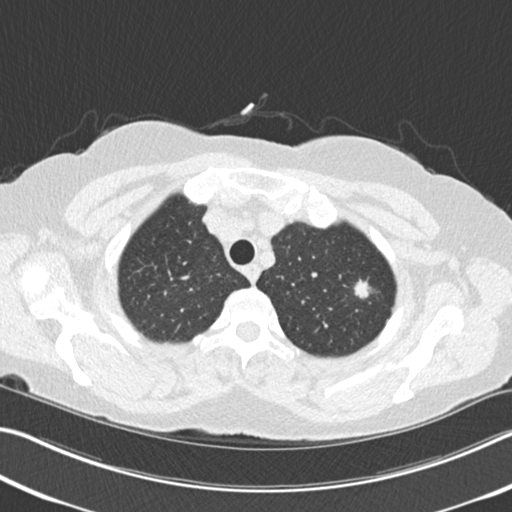
Low-dose screening chest CT, one axial slice. Reconstruction kernel B30f. 120 kVp. Lung window (W 1500 / L -600 HU). 512 × 512 image matrix, field of view 342 × 342 mm.
Structures marked on this image (manually delineated by an expert):
- lesion 1 (tumor): bounding box (x1, y1, x2, y2) in pixels: (354, 279, 371, 299)